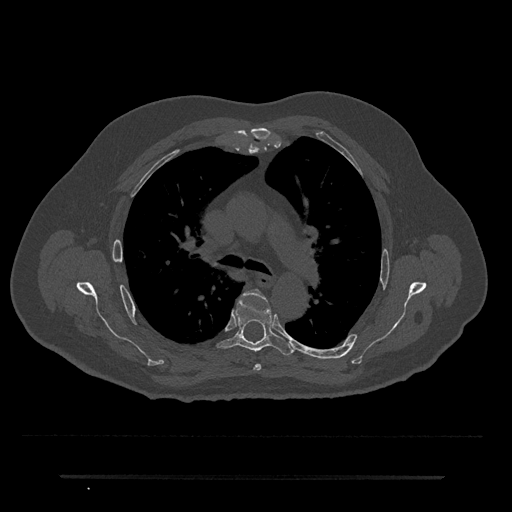
CT including the spine, one axial slice. Slice 491 of 797 in the series (ordered by position). Reconstruction kernel Br40s/3. 120 kVp. Bone window (W 1800 / L 400 HU). 0.5 mm slice thickness. 512 × 512 image matrix. Male patient, age 69 years. From the clinical record (not read from this slice): primary cancer: prostate.
Outlined on this slice (semi-automatic segmentation, software-assisted and operator-edited):
- T4 vertebra: box from (x=243, y=289) to (x=267, y=371) px
- T5 vertebra: (x=216, y=295)–(x=294, y=355)